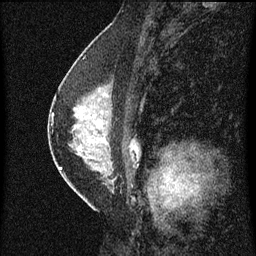
Breast MRI (dynamic contrast-enhanced), one sagittal slice; position 34 of 60 along the scan axis; dynamic contrast-enhanced series, image 2 of 3 at this slice position (ordered by acquisition); 1.5 T; TE 4.2 ms, TR 8 ms; 2 mm slice thickness; 256 × 256 image matrix, field of view 180 × 180 mm. Patient: female, 47 years.
Annotated regions visible in this slice (semi-automatically segmented with operator editing):
- analysis volume of interest (the breast-tissue region the enhancement analysis was run in; not a lesion): box from (x=54, y=80) to (x=139, y=187) px
- tumour enhancement mask (voxels above the 70 % enhancement threshold inside the analysis volume of interest): (x=60, y=168)–(x=63, y=171)